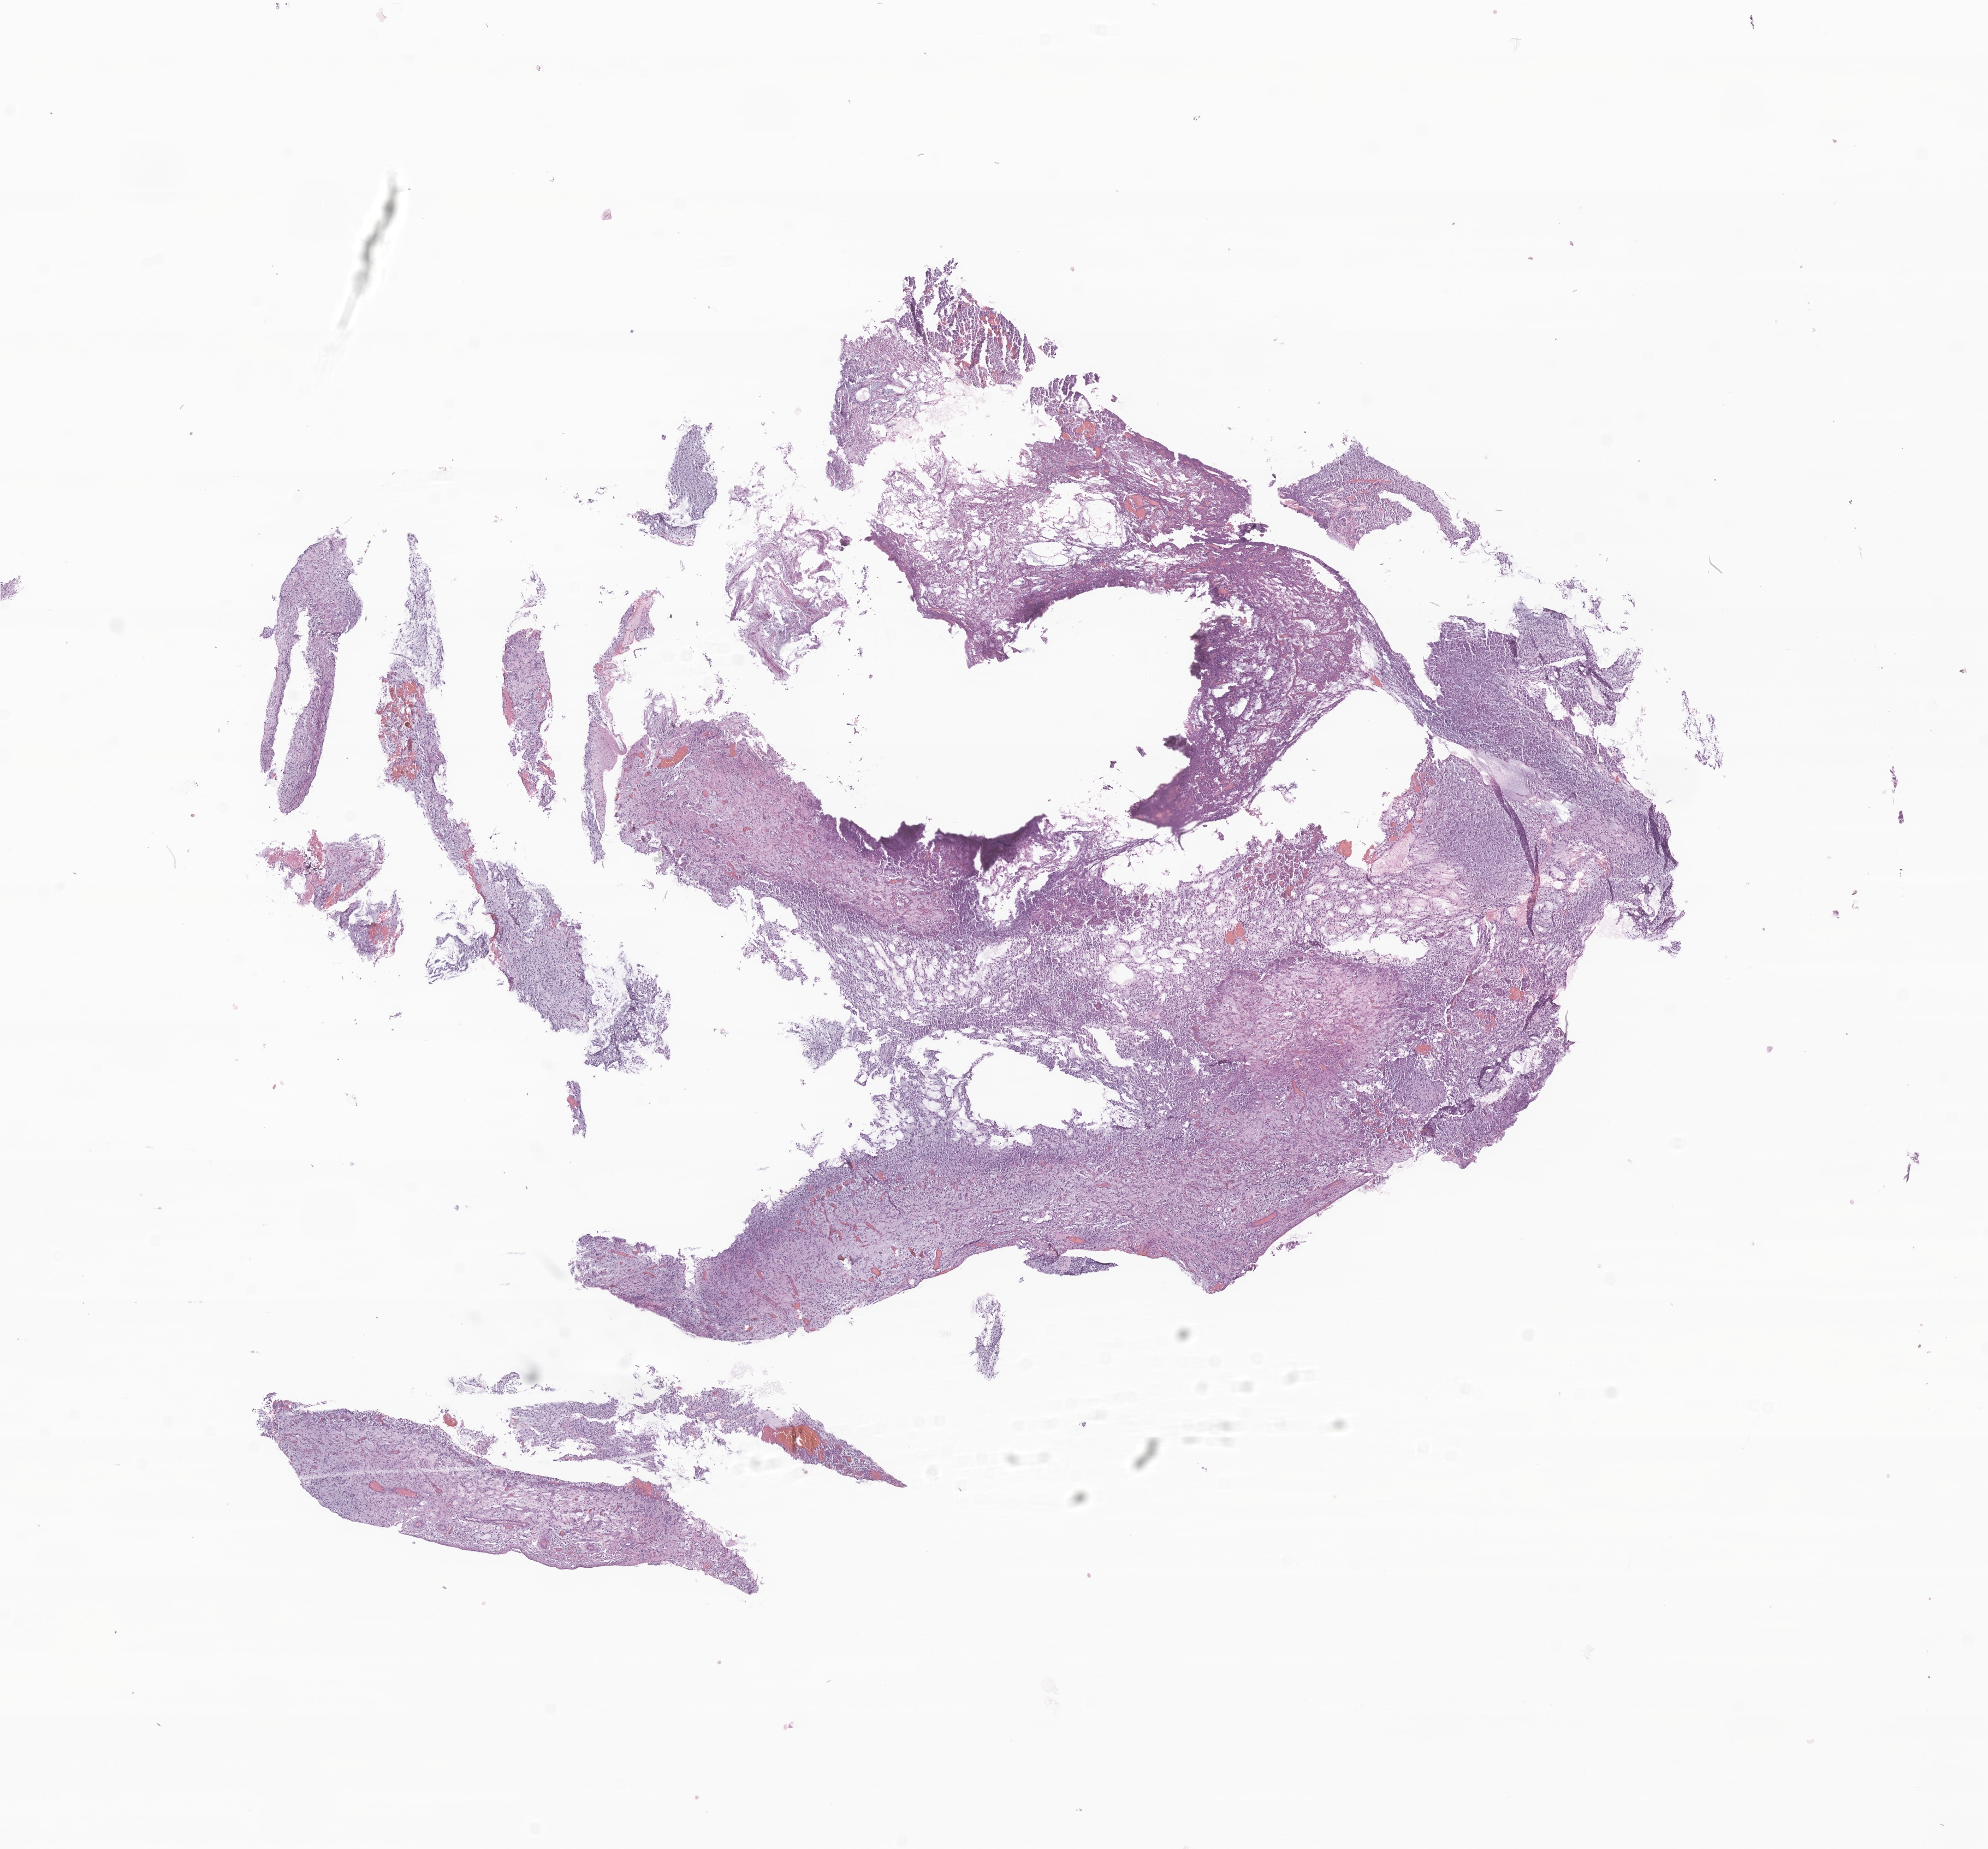
Whole-slide image, haematoxylin and eosin stain of tumor tissue from the brain — whole scanned area (about 15.3 x 14.3 mm) shown as a low-resolution overview. Formalin-fixed paraffin-embedded section. Patient: male, age 197 days.
Diagnosis: Glioma, malignant.